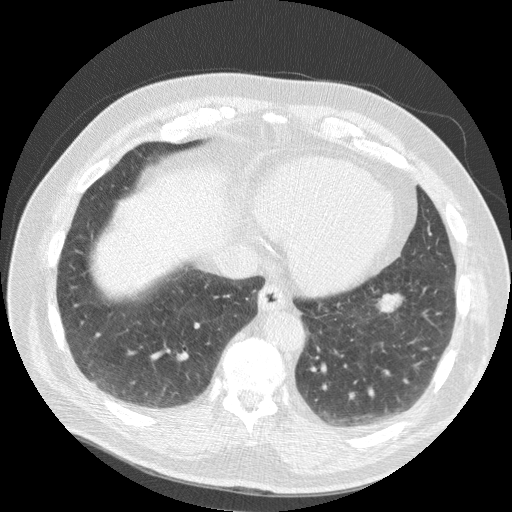
Axial slice from a low-dose chest CT screening exam, second annual screen, lung window (W 1500 / L -600 HU), 120 kVp, slice 70 of 188 in the series. Male participant, aged 63 years at enrolment.
- Expert reader's lesion annotation, bounding box <362,283,410,323> (left, top, right, bottom; pixels).
- The screening reader recorded 2 non-calcified nodules or masses ≥4 mm on this exam (right middle lobe, left lower lobe); which of them this box marks is not recorded.
- Lung cancer was diagnosed 633 days after this screen (after the third annual screen): squamous cell carcinoma, NOS, left lower lobe, stage IB (AJCC 6th edition), 48 mm at pathology.